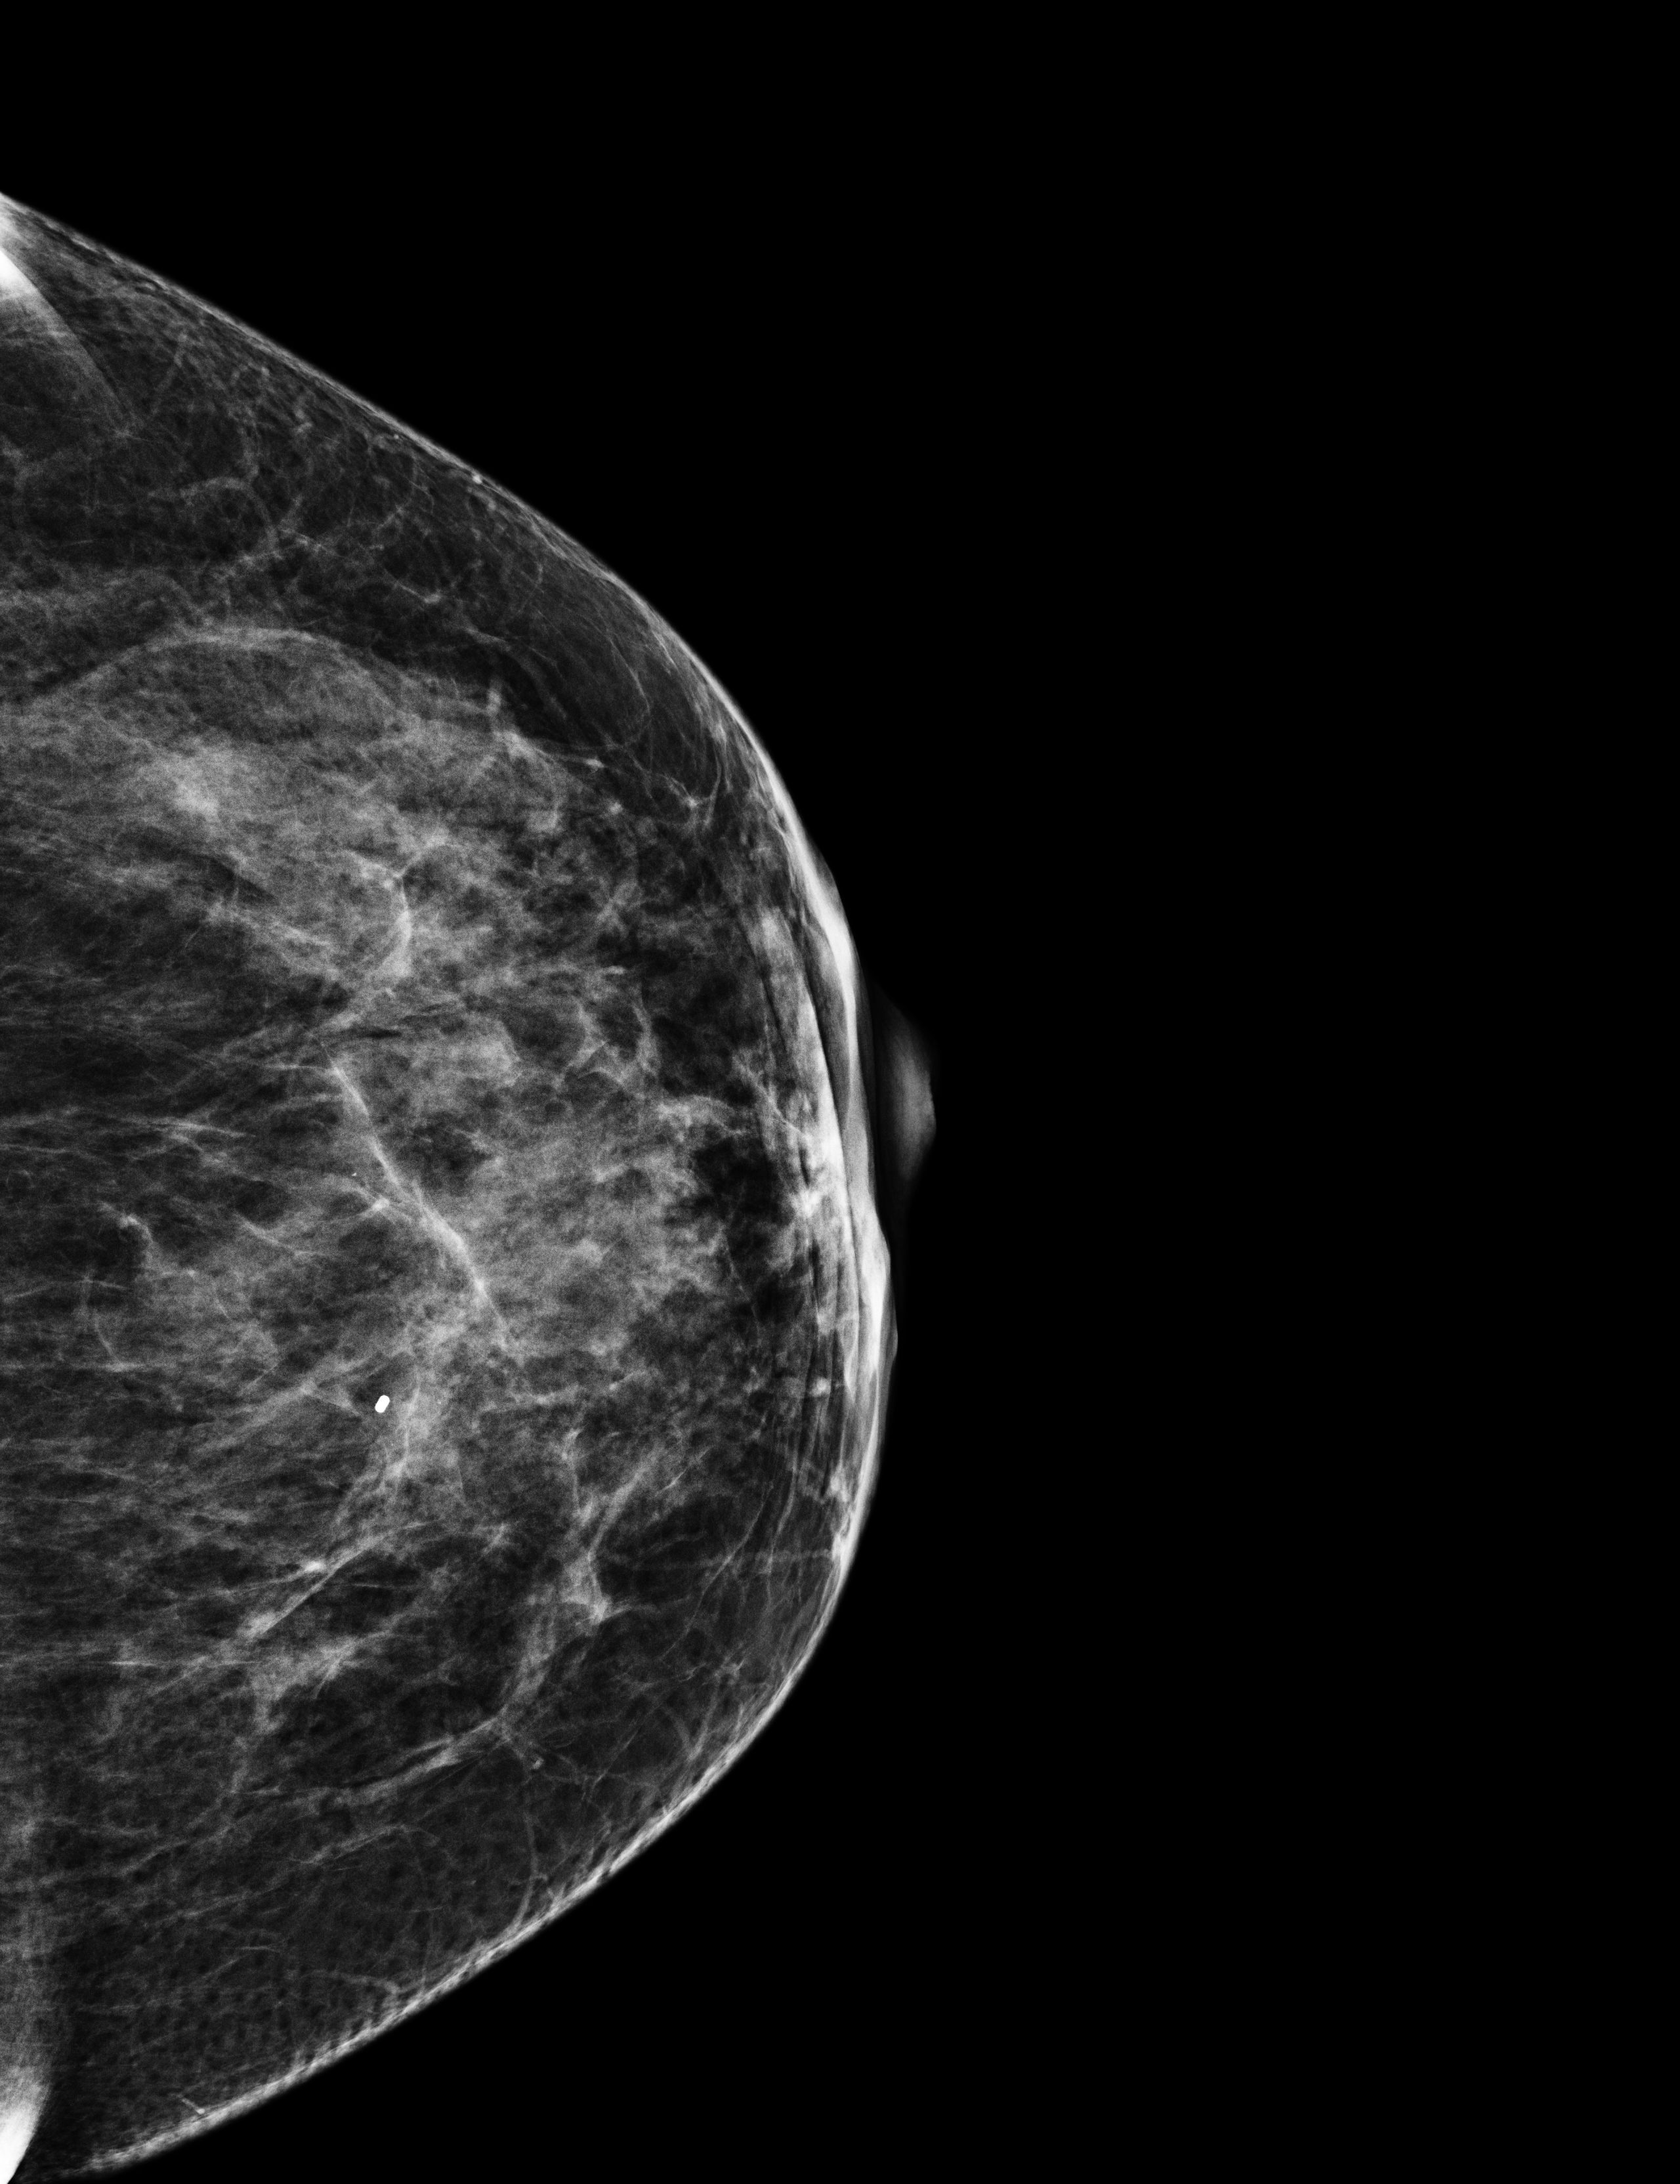
Full-field digital mammogram (FFDM), left breast, cranio-caudal projection, annual screening mammography examination, compressed breast thickness 50 mm, system: Selenia Dimensions. Patient aged 42 years (female).
BI-RADS breast density category at the screening exam (both breasts, scale 1–4): 3. Final BI-RADS assessment for this screening round (tomosynthesis exam, both breasts): category 1. Recall: no recall after this screen.